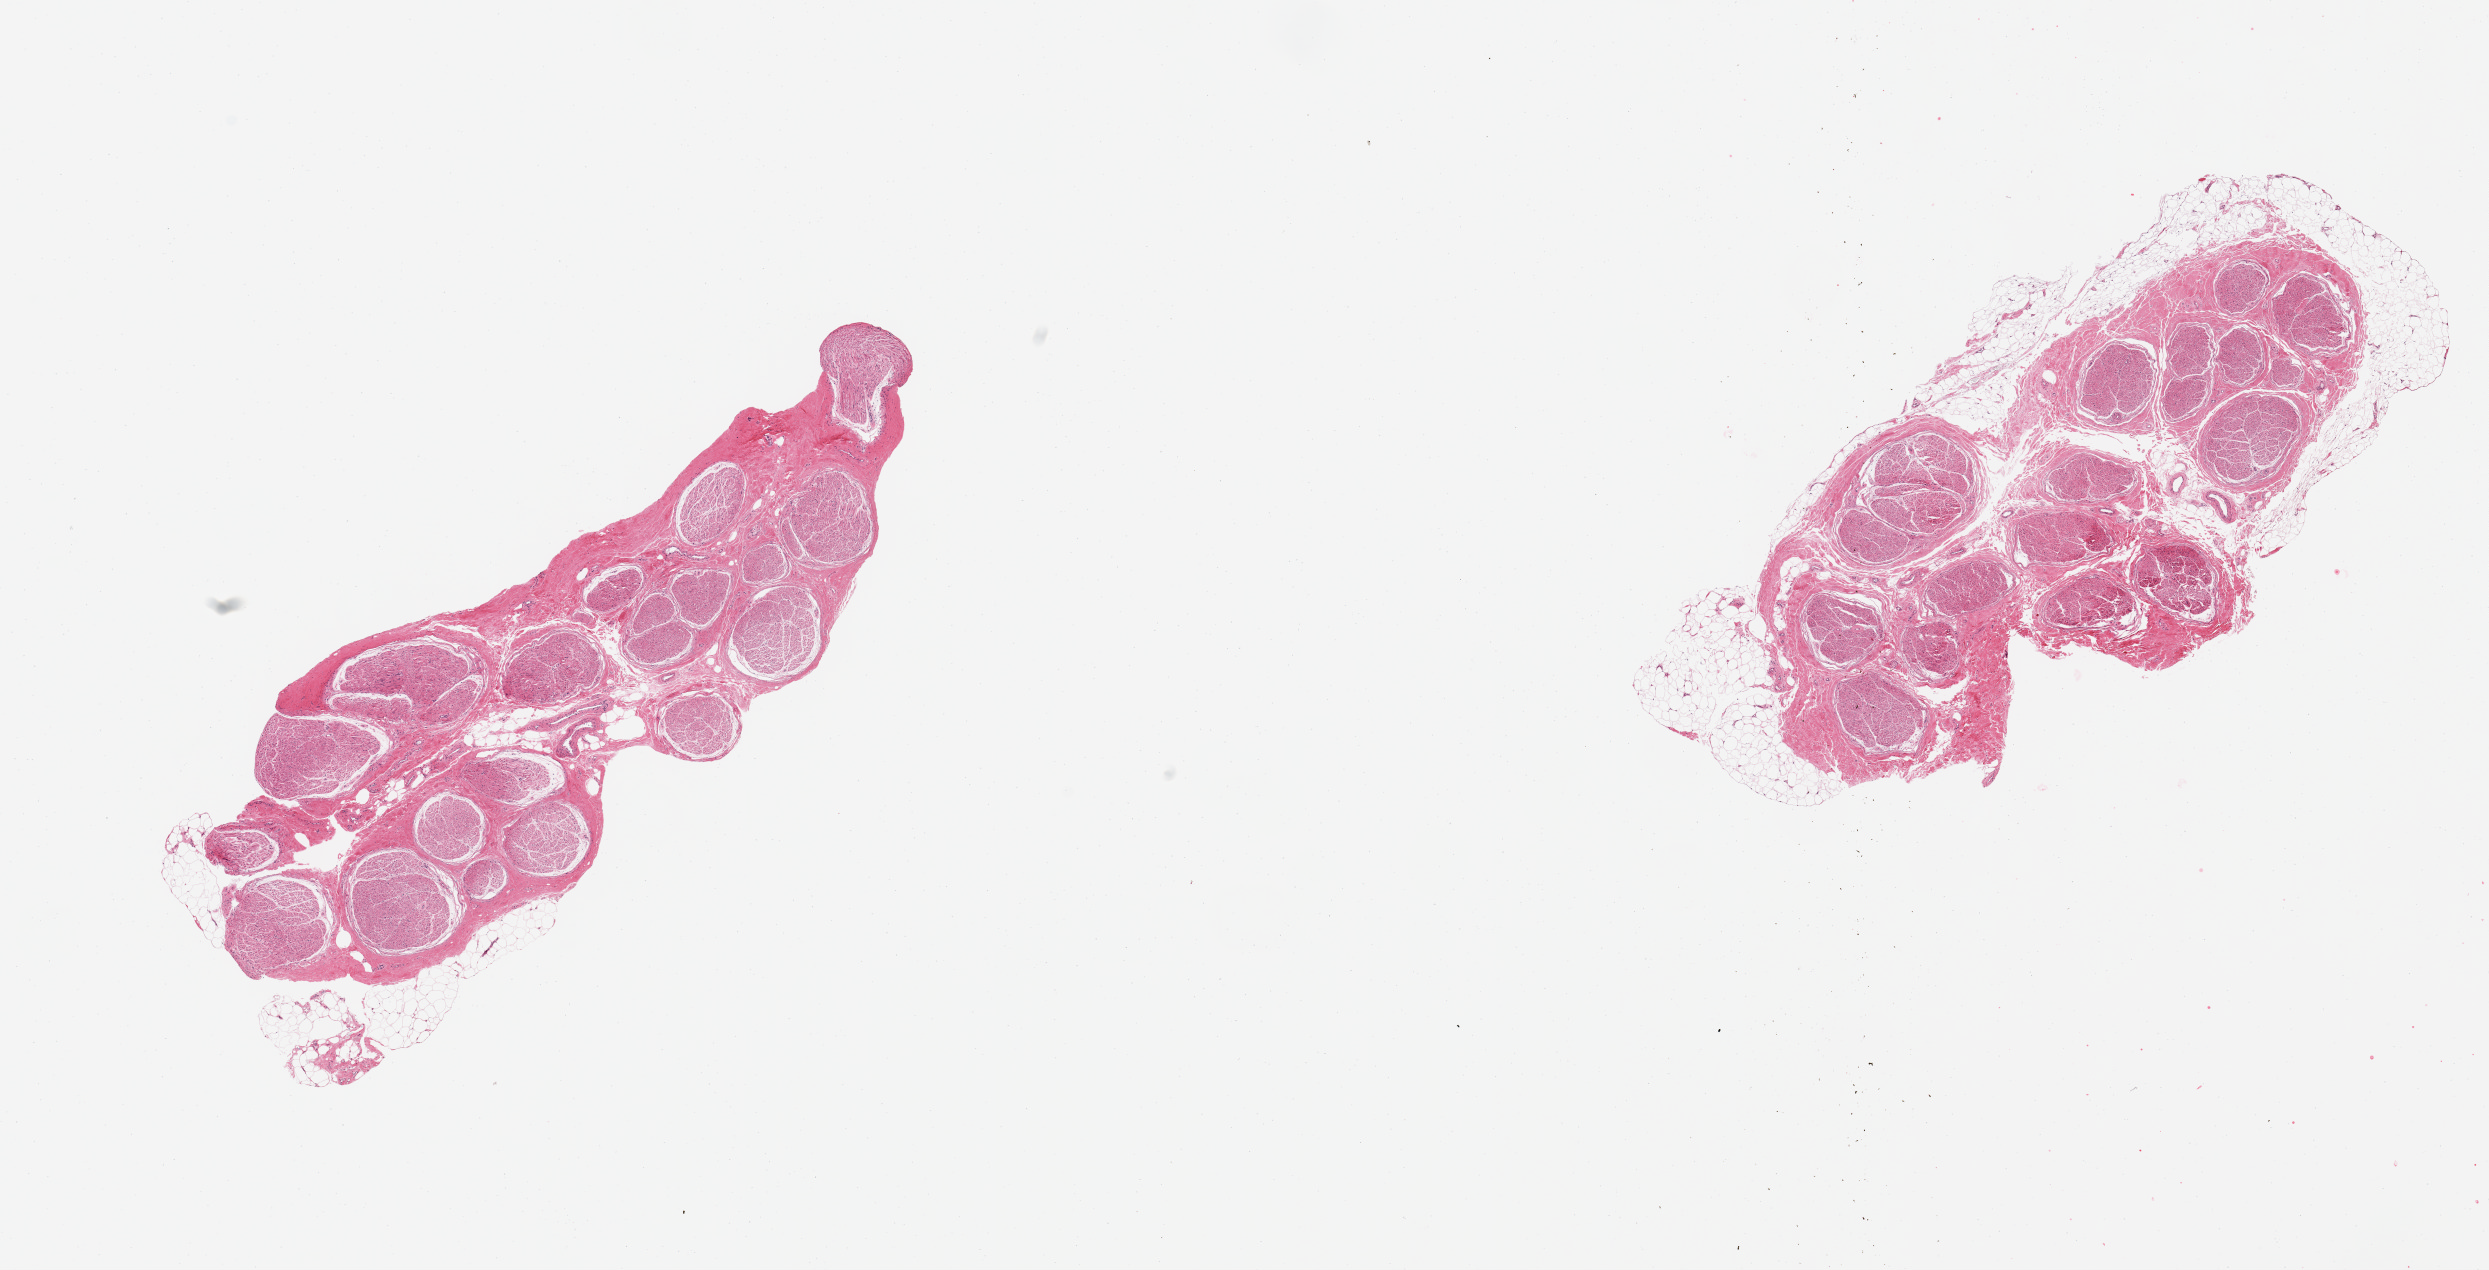
Whole-slide image, haematoxylin and eosin stain — low-resolution overview of the scanned area, about 19.7 x 10.0 mm. PAXgene-fixed, paraffin-embedded tissue. Section of tibial nerve (target tissue). Donor tissue sample.
• review note (as recorded): 2 pieces, partial rims of adherent fat up to ~0.7mm